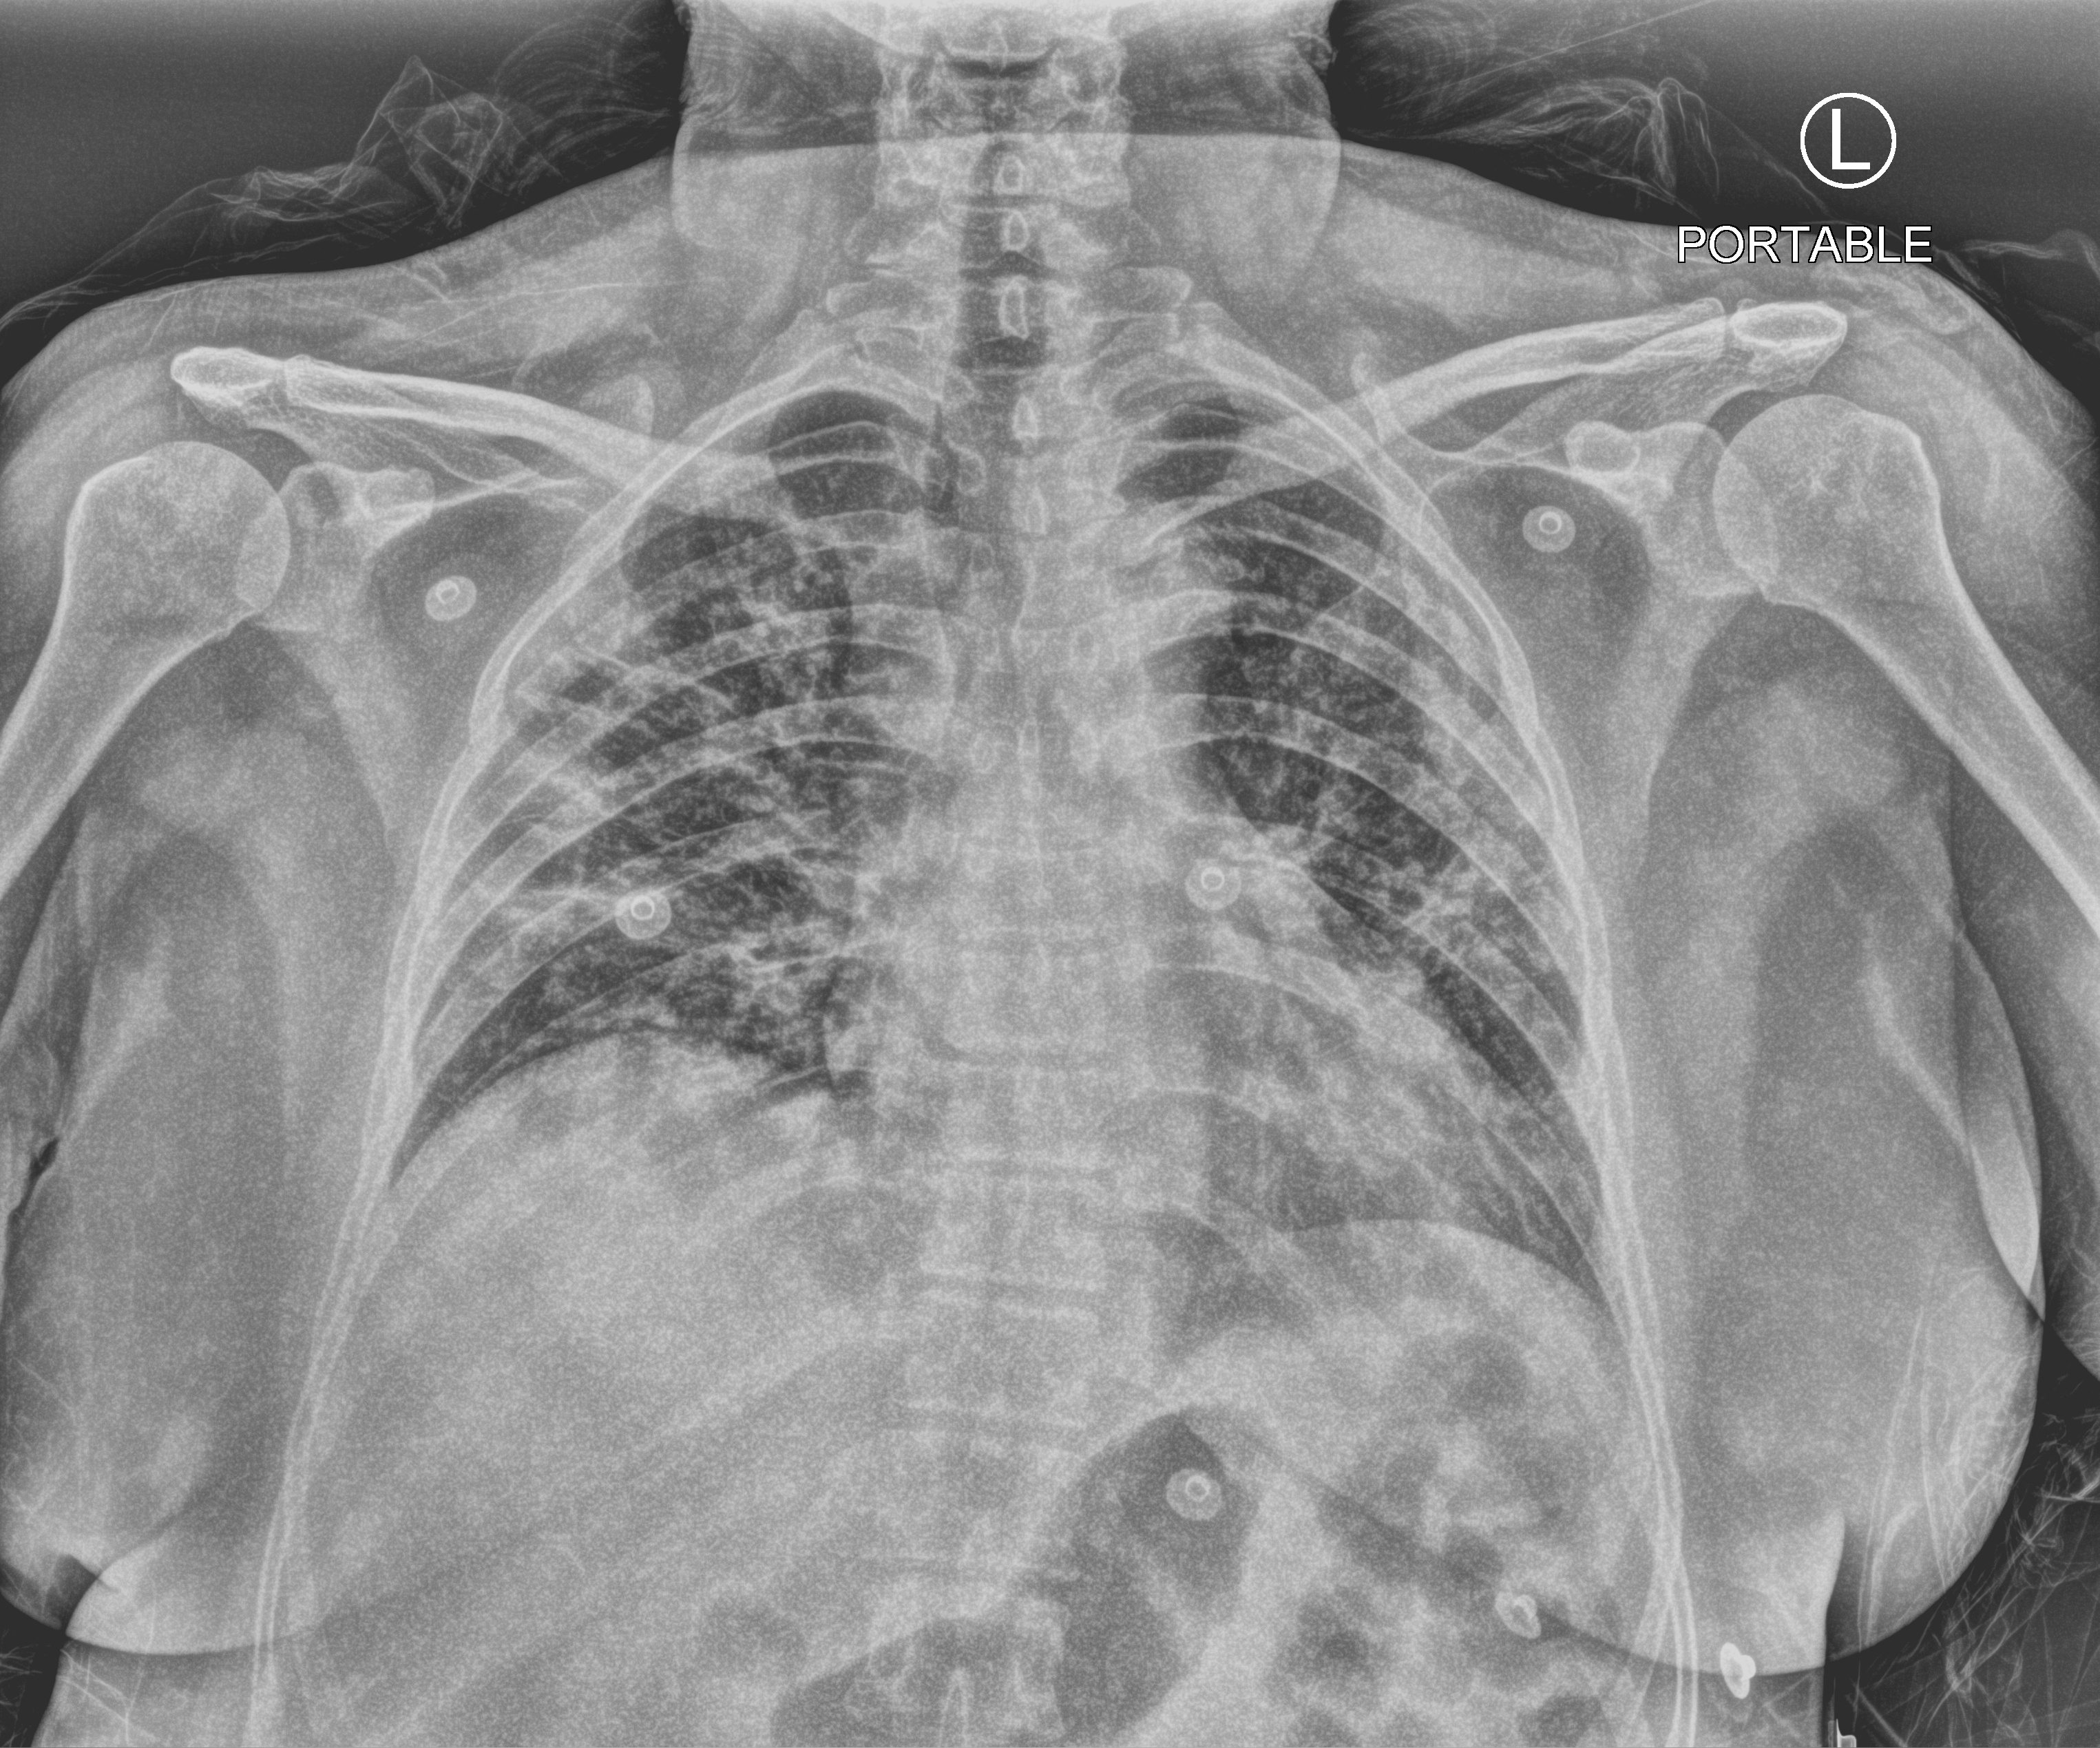
Portable chest radiograph, anteroposterior (AP) projection. Patient hospitalised with COVID-19; female, aged 60–74 years.
Hospital-stay facts (about this admission, not read from this image; timing relative to this image not recorded): admitted to intensive care during this hospital stay: no; COPD (admission record): no.